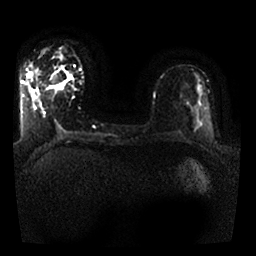
Breast MRI, one axial slice. Position 9 of 25 along the scan axis. Diffusion-weighted series; image 2 of 4 stored at this slice position (different b-values; order by instance number). 1.5 T. 4 mm slice thickness. 256 × 256 image matrix, field of view 330 × 330 mm. Female patient.
Annotated regions visible in this slice (outlined manually by an expert reader):
- tumour on diffusion-weighted imaging: bounding box (x1, y1, x2, y2) in pixels: (53, 85, 63, 91)